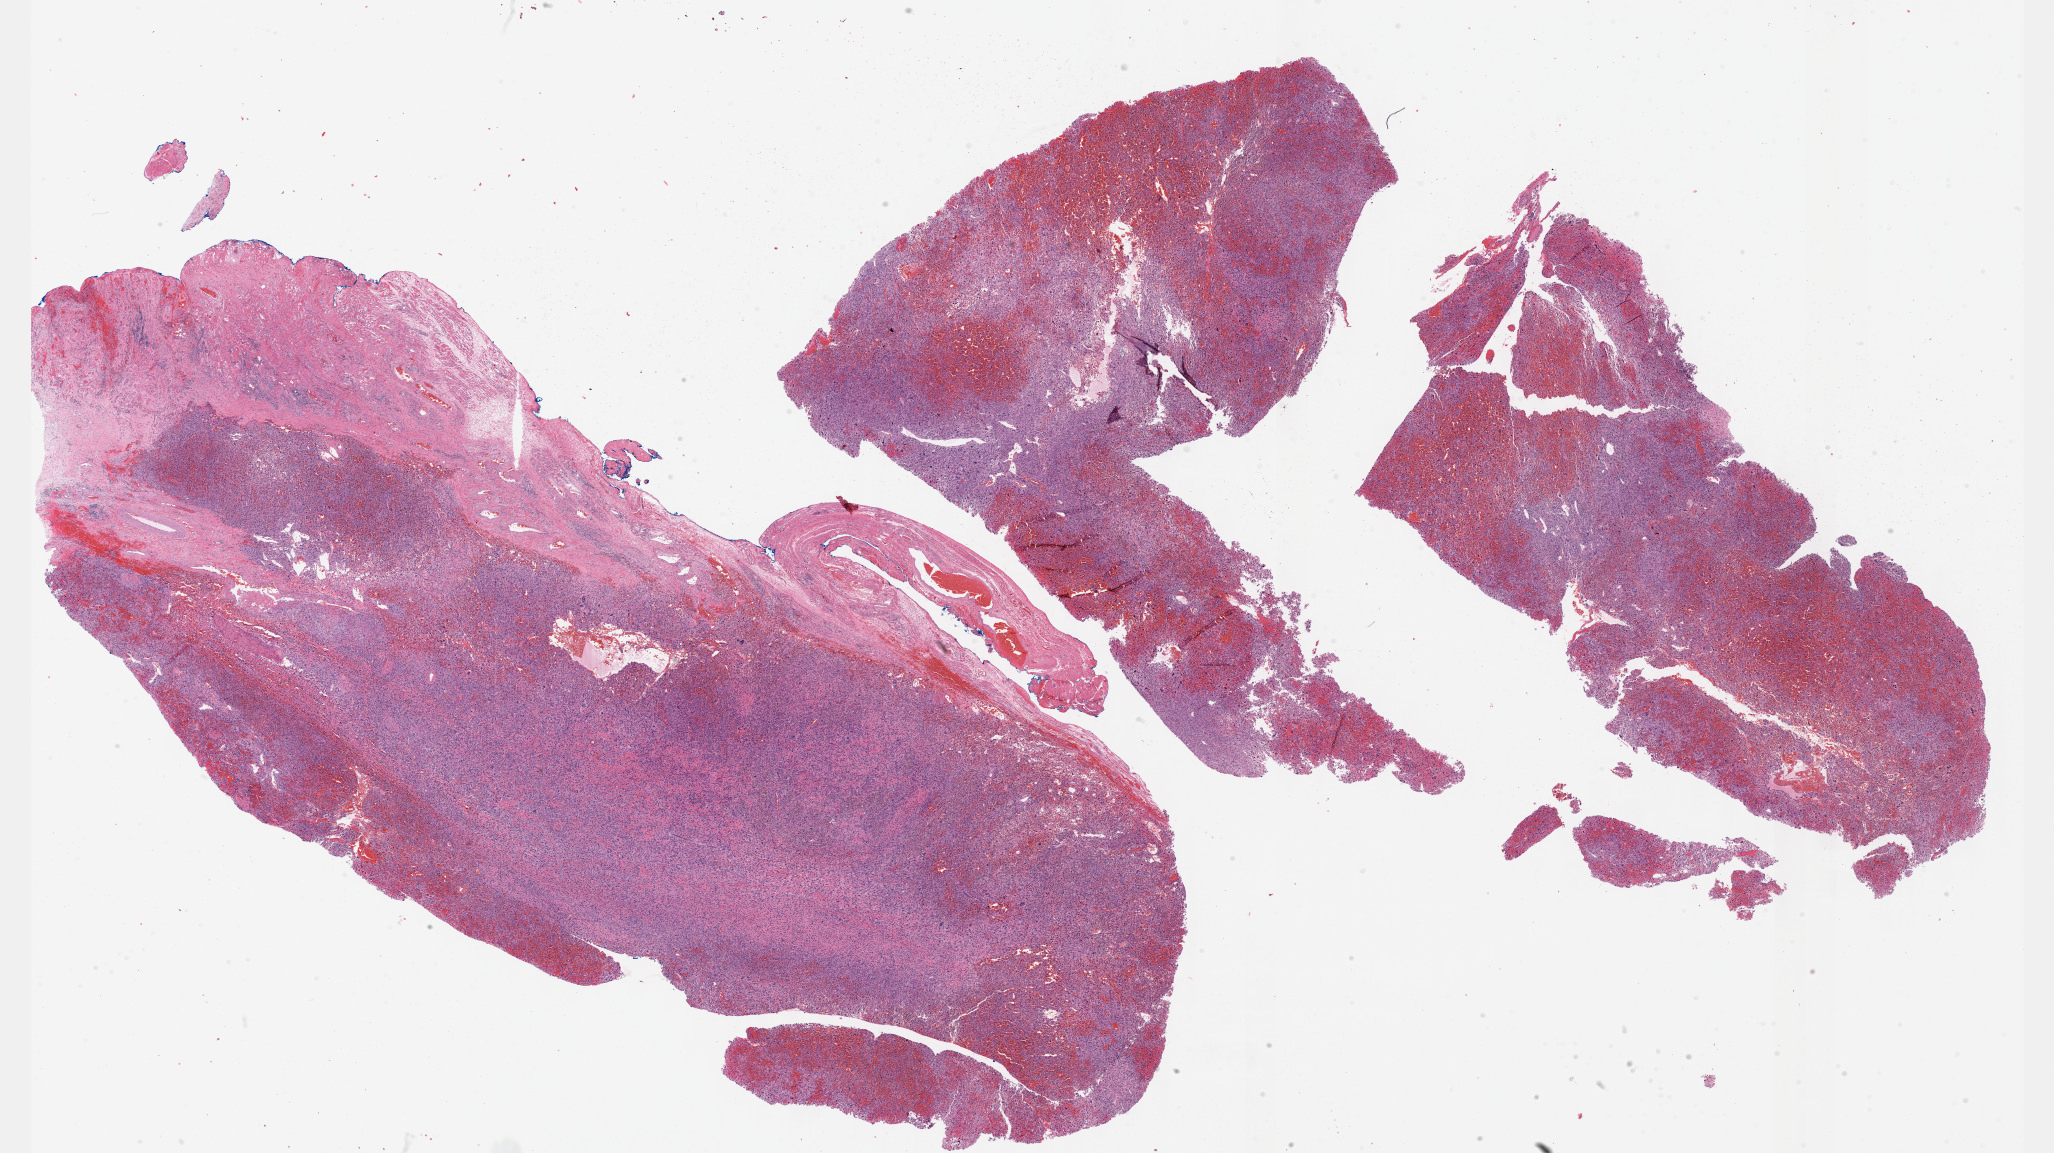
Whole-slide histology image, Hematoxylin and eosin (H&E) stained — a low-resolution overview of the entire scanned area, about 33.2 x 18.6 mm (acquisition: 40x scan), formalin-fixed paraffin-embedded (FFPE) diagnostic section, sample: primary tumour, connective, subcutaneous and other soft tissues. Patient: male, age at initial diagnosis 56 years.
• pathologic diagnosis: Undifferentiated sarcoma (connective, subcutaneous and other soft tissues of lower limb and hip)